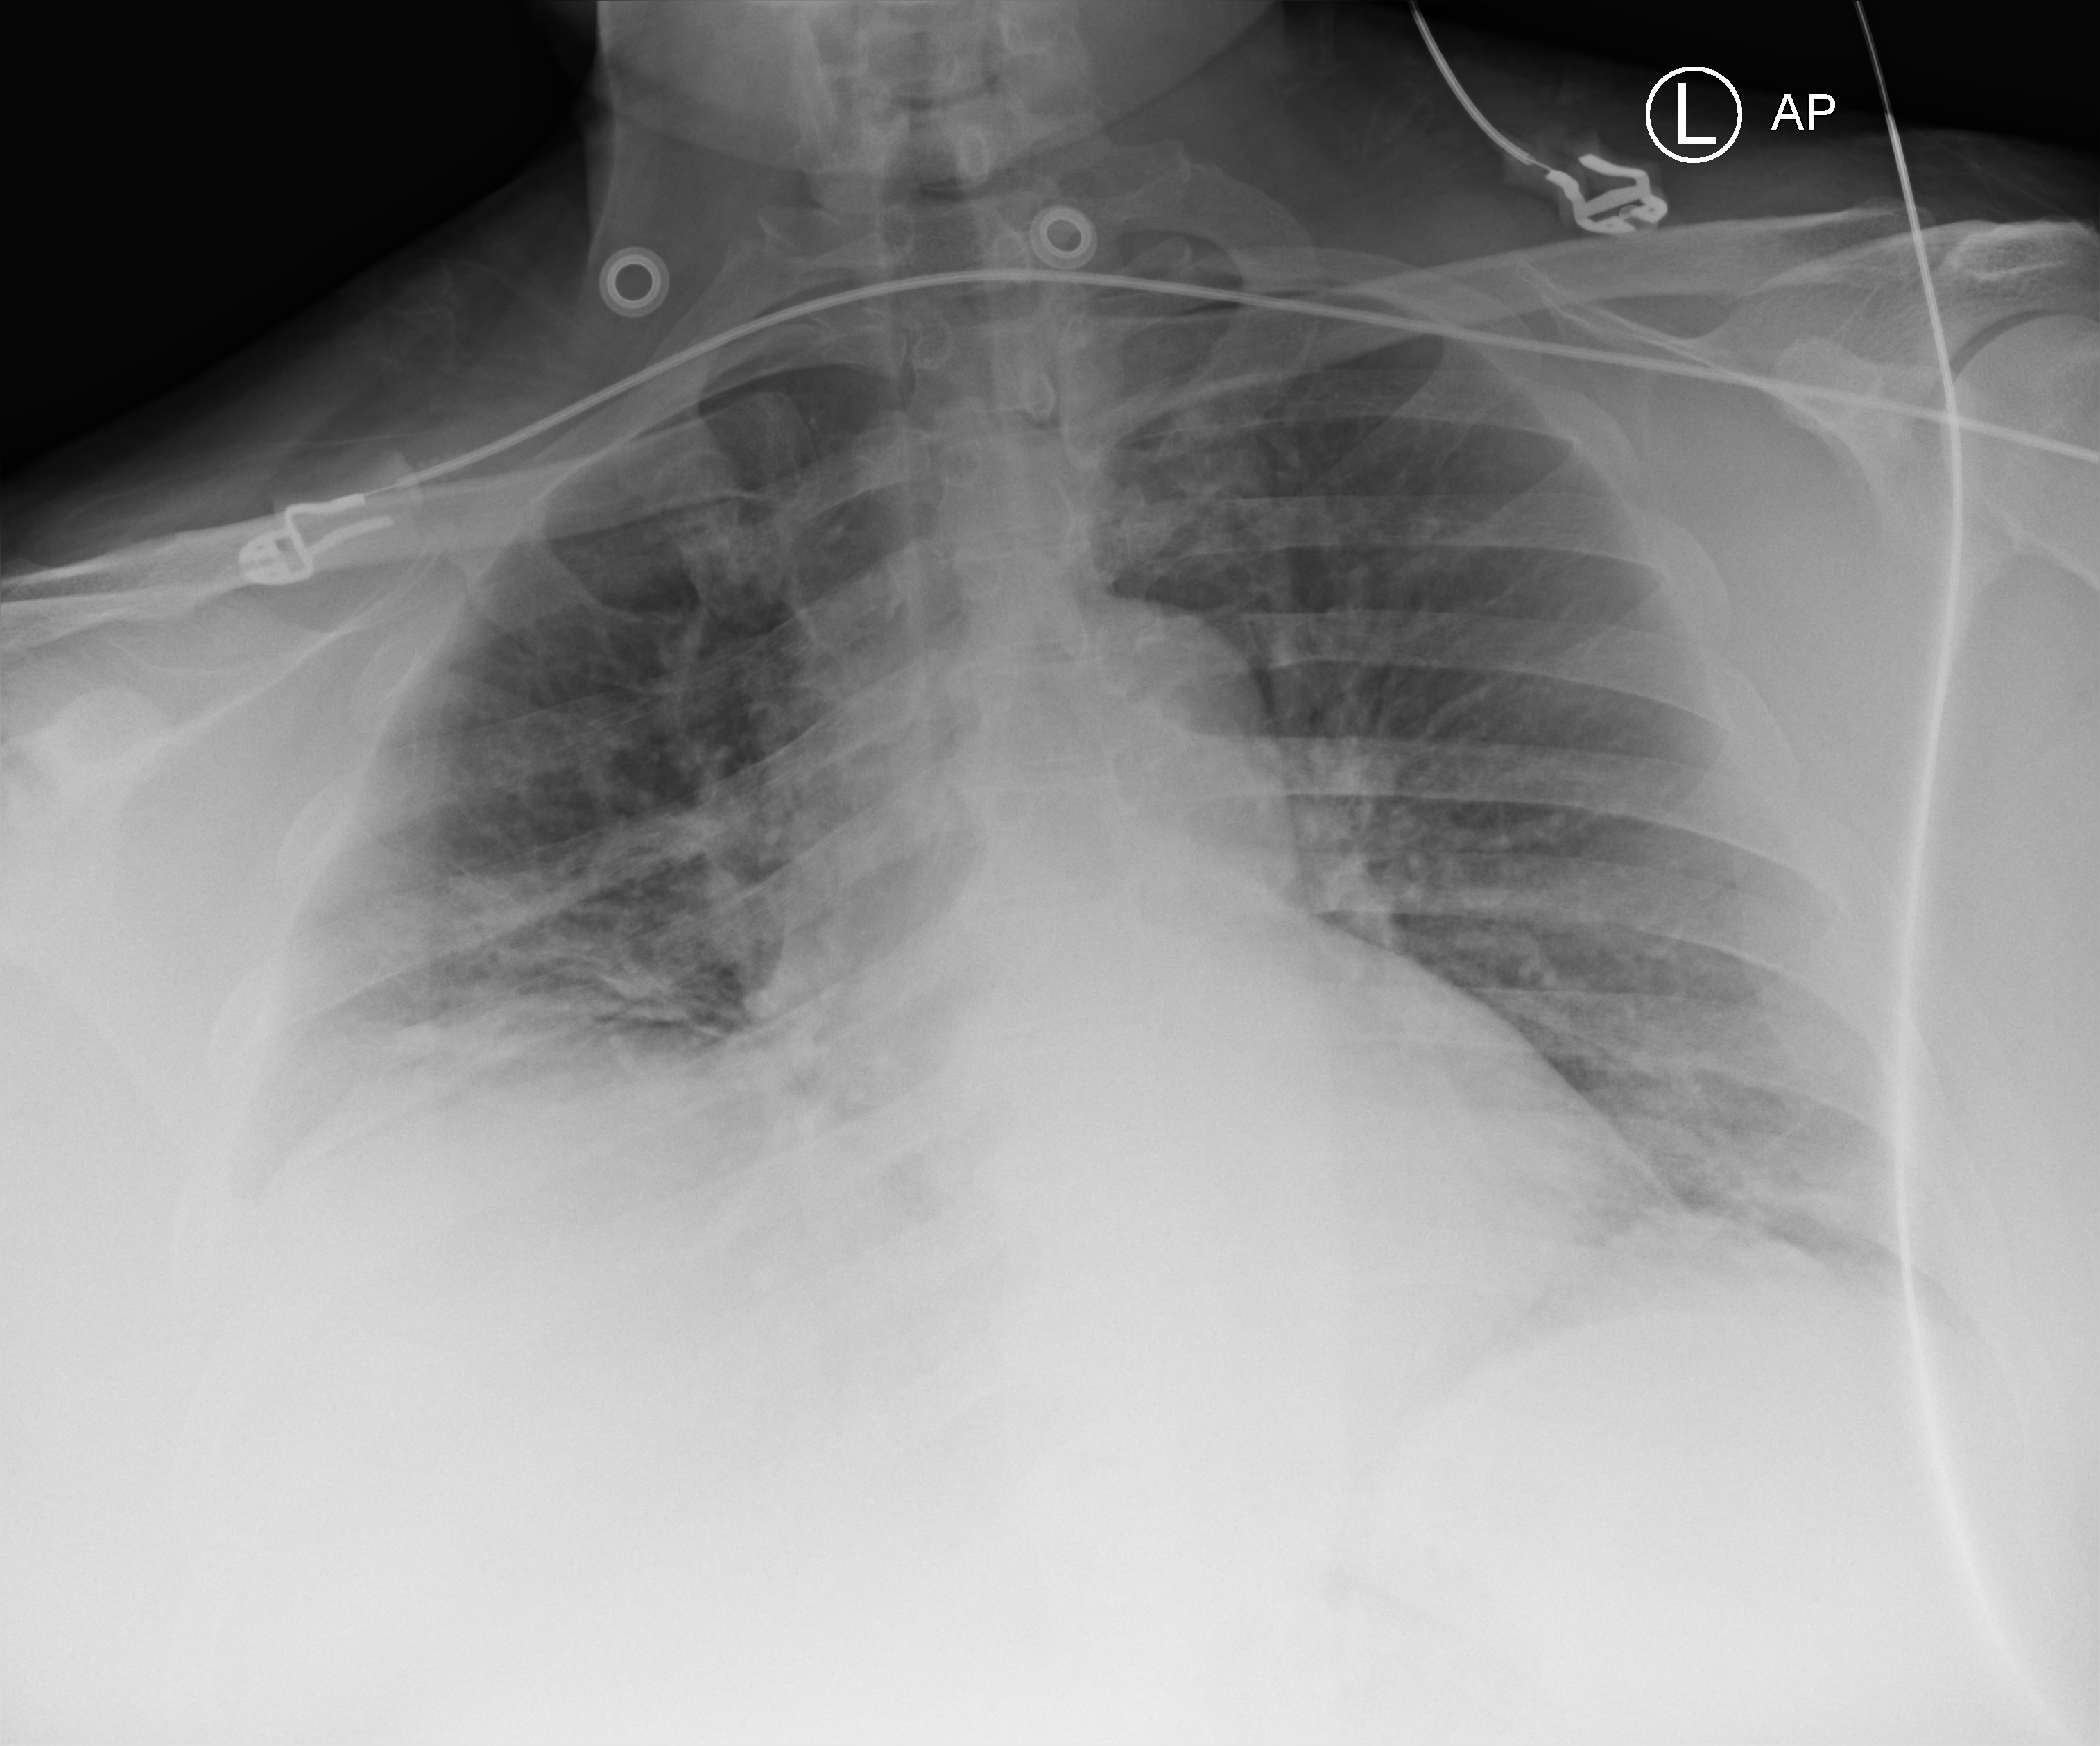
Portable chest radiograph, anteroposterior (AP) projection. Male patient hospitalised with COVID-19, age 18–59 years.
Admission-level facts for this patient (not findings on this image; timing relative to this image not recorded): length of hospital stay: 8 days; other chronic lung disease (admission record): no; mechanically ventilated during this hospital stay: no.